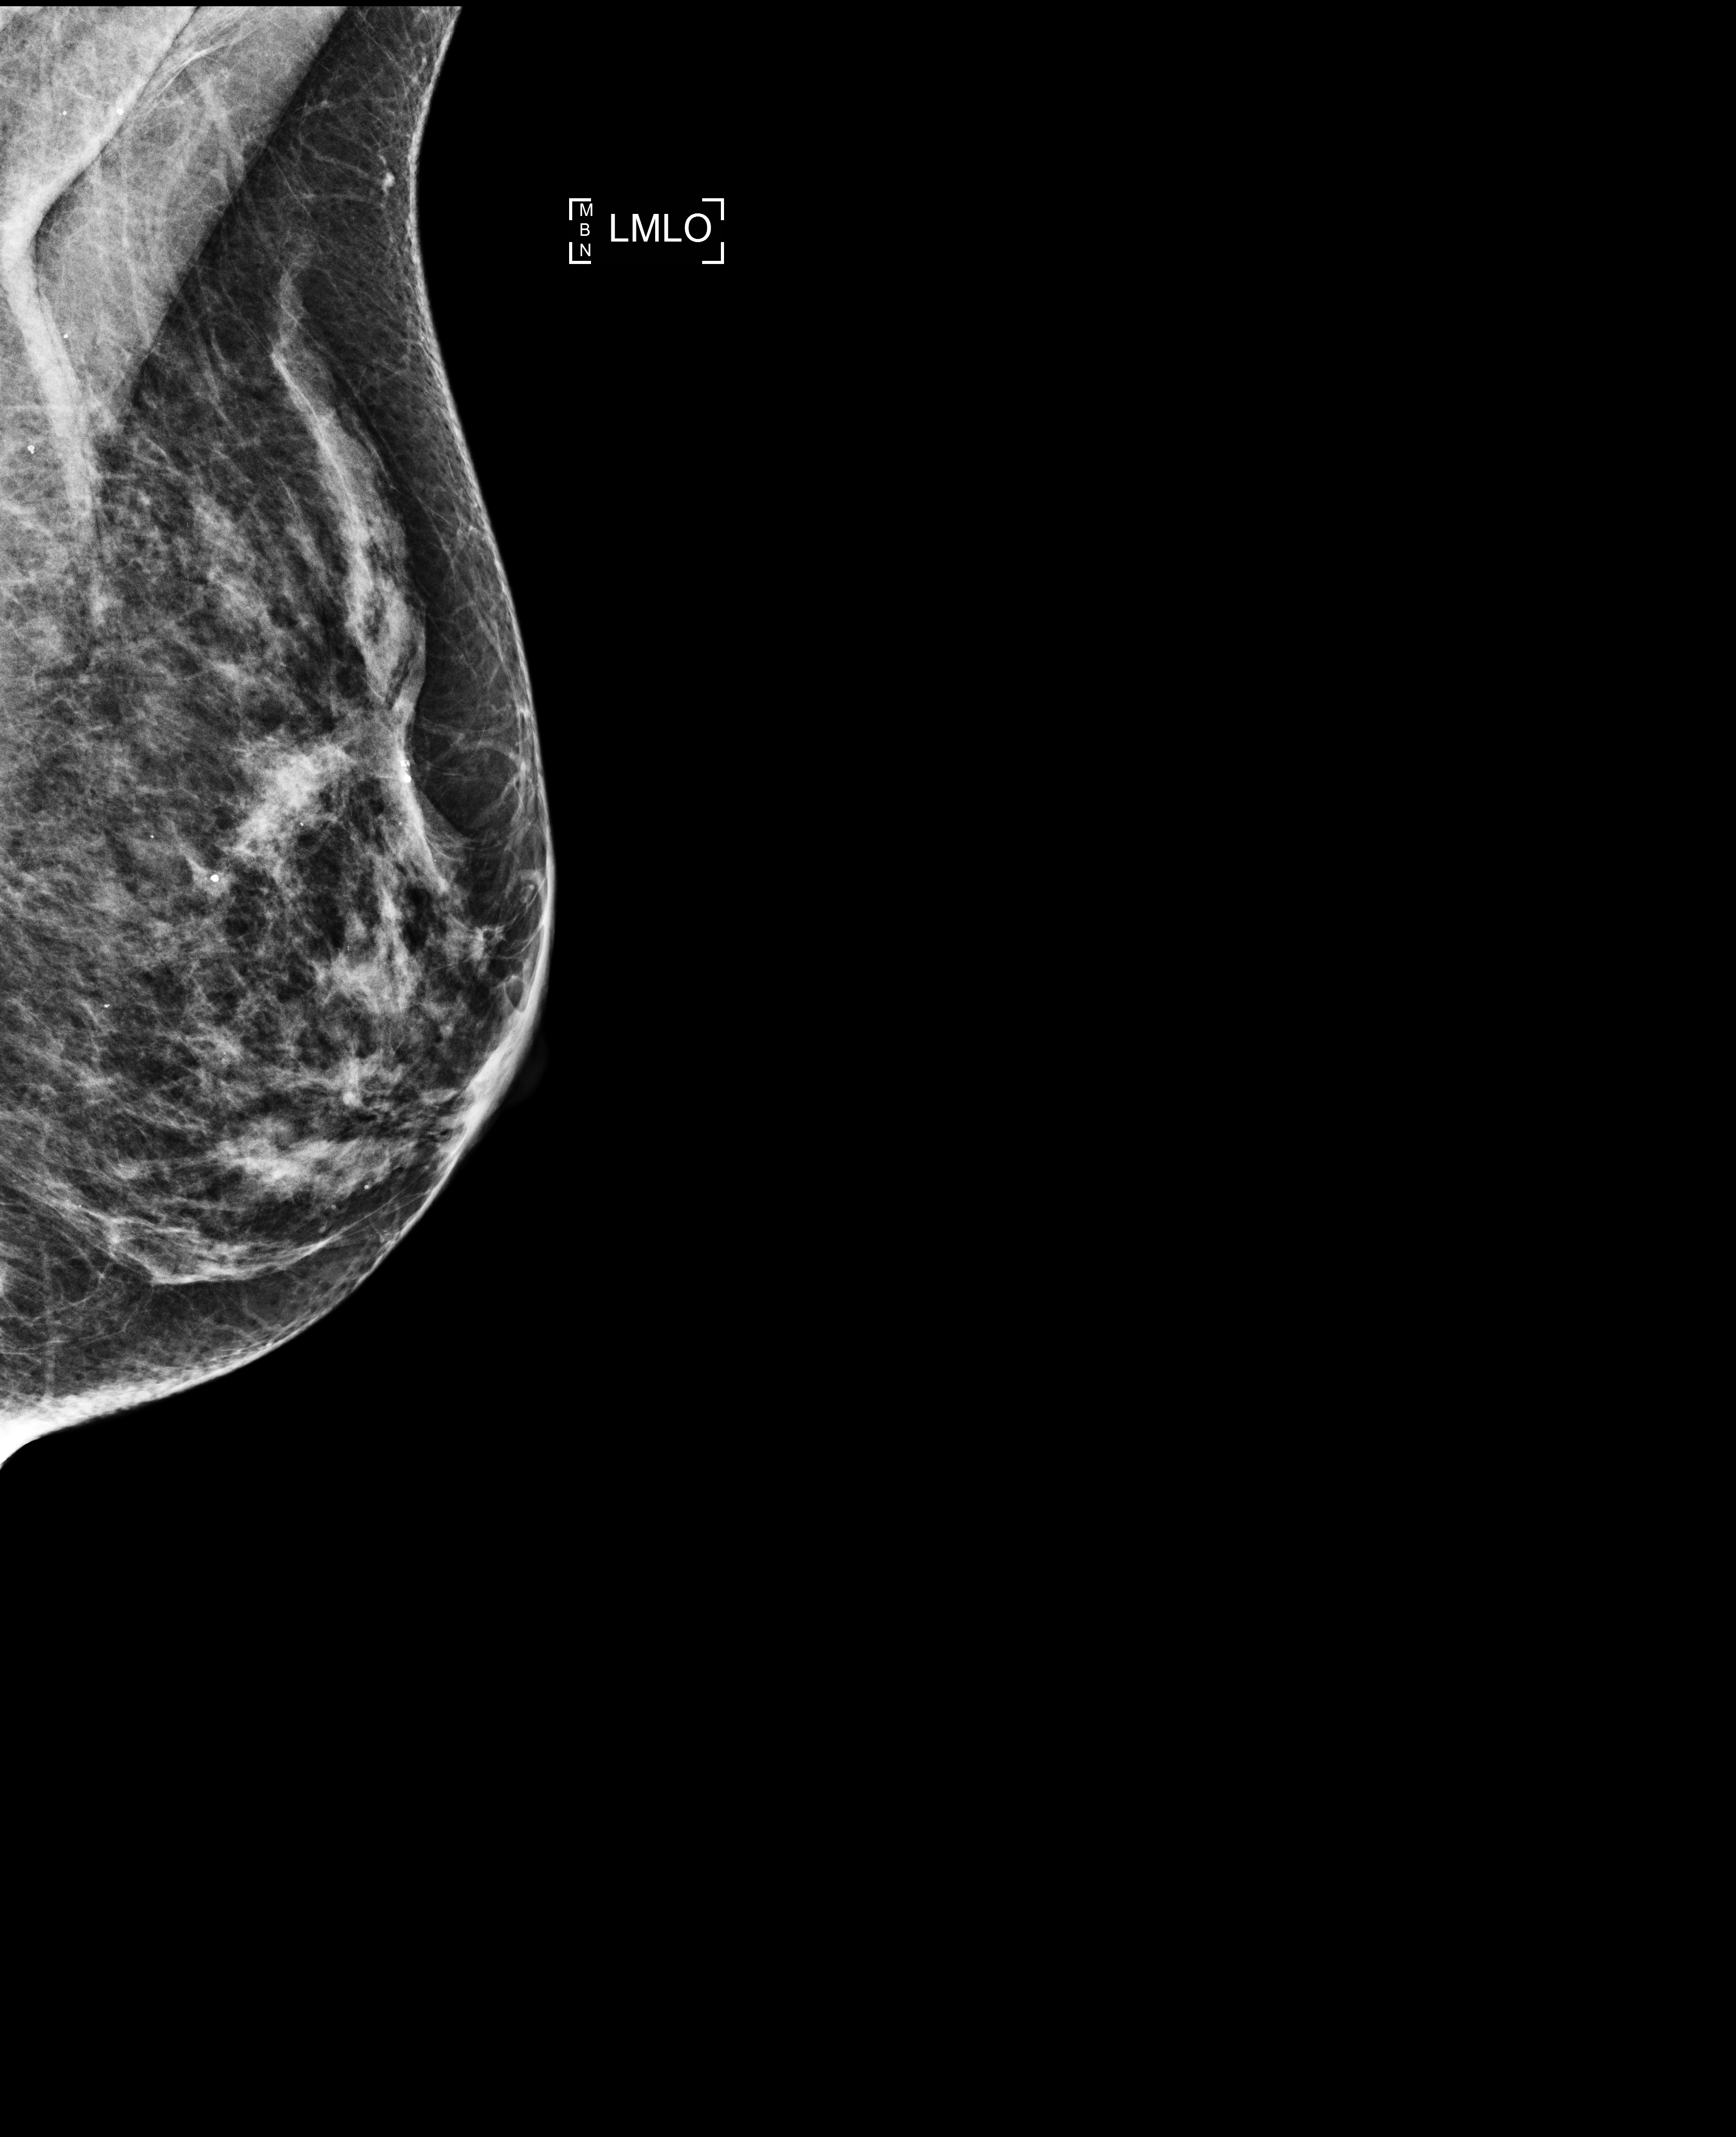
Annual screening mammography examination, system: Selenia Dimensions. Patient aged 75 years (female).
Image type: full-field digital mammogram. Breast: left. Projection: MLO view.